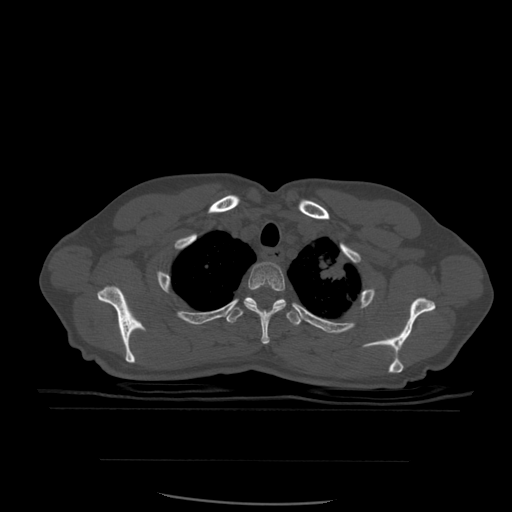
CT including the spine, one axial slice; slice 452 of 574 in the series (ordered by position); bone window (W 1800 / L 400 HU); 1.25 mm slice thickness; 512 × 512 image matrix, field of view 392 × 392 mm. Patient age 48 years. Case-level facts recorded for this patient, not image findings: primary cancer: lung; vertebrae with lytic lesions (as recorded): T11.
Outlined on this slice (semi-automatic segmentation, software-assisted and operator-edited):
- T2 vertebra: bounding box <244,262,286,345> (left, top, right, bottom; pixels)
- T3 vertebra: <226,297,304,326>